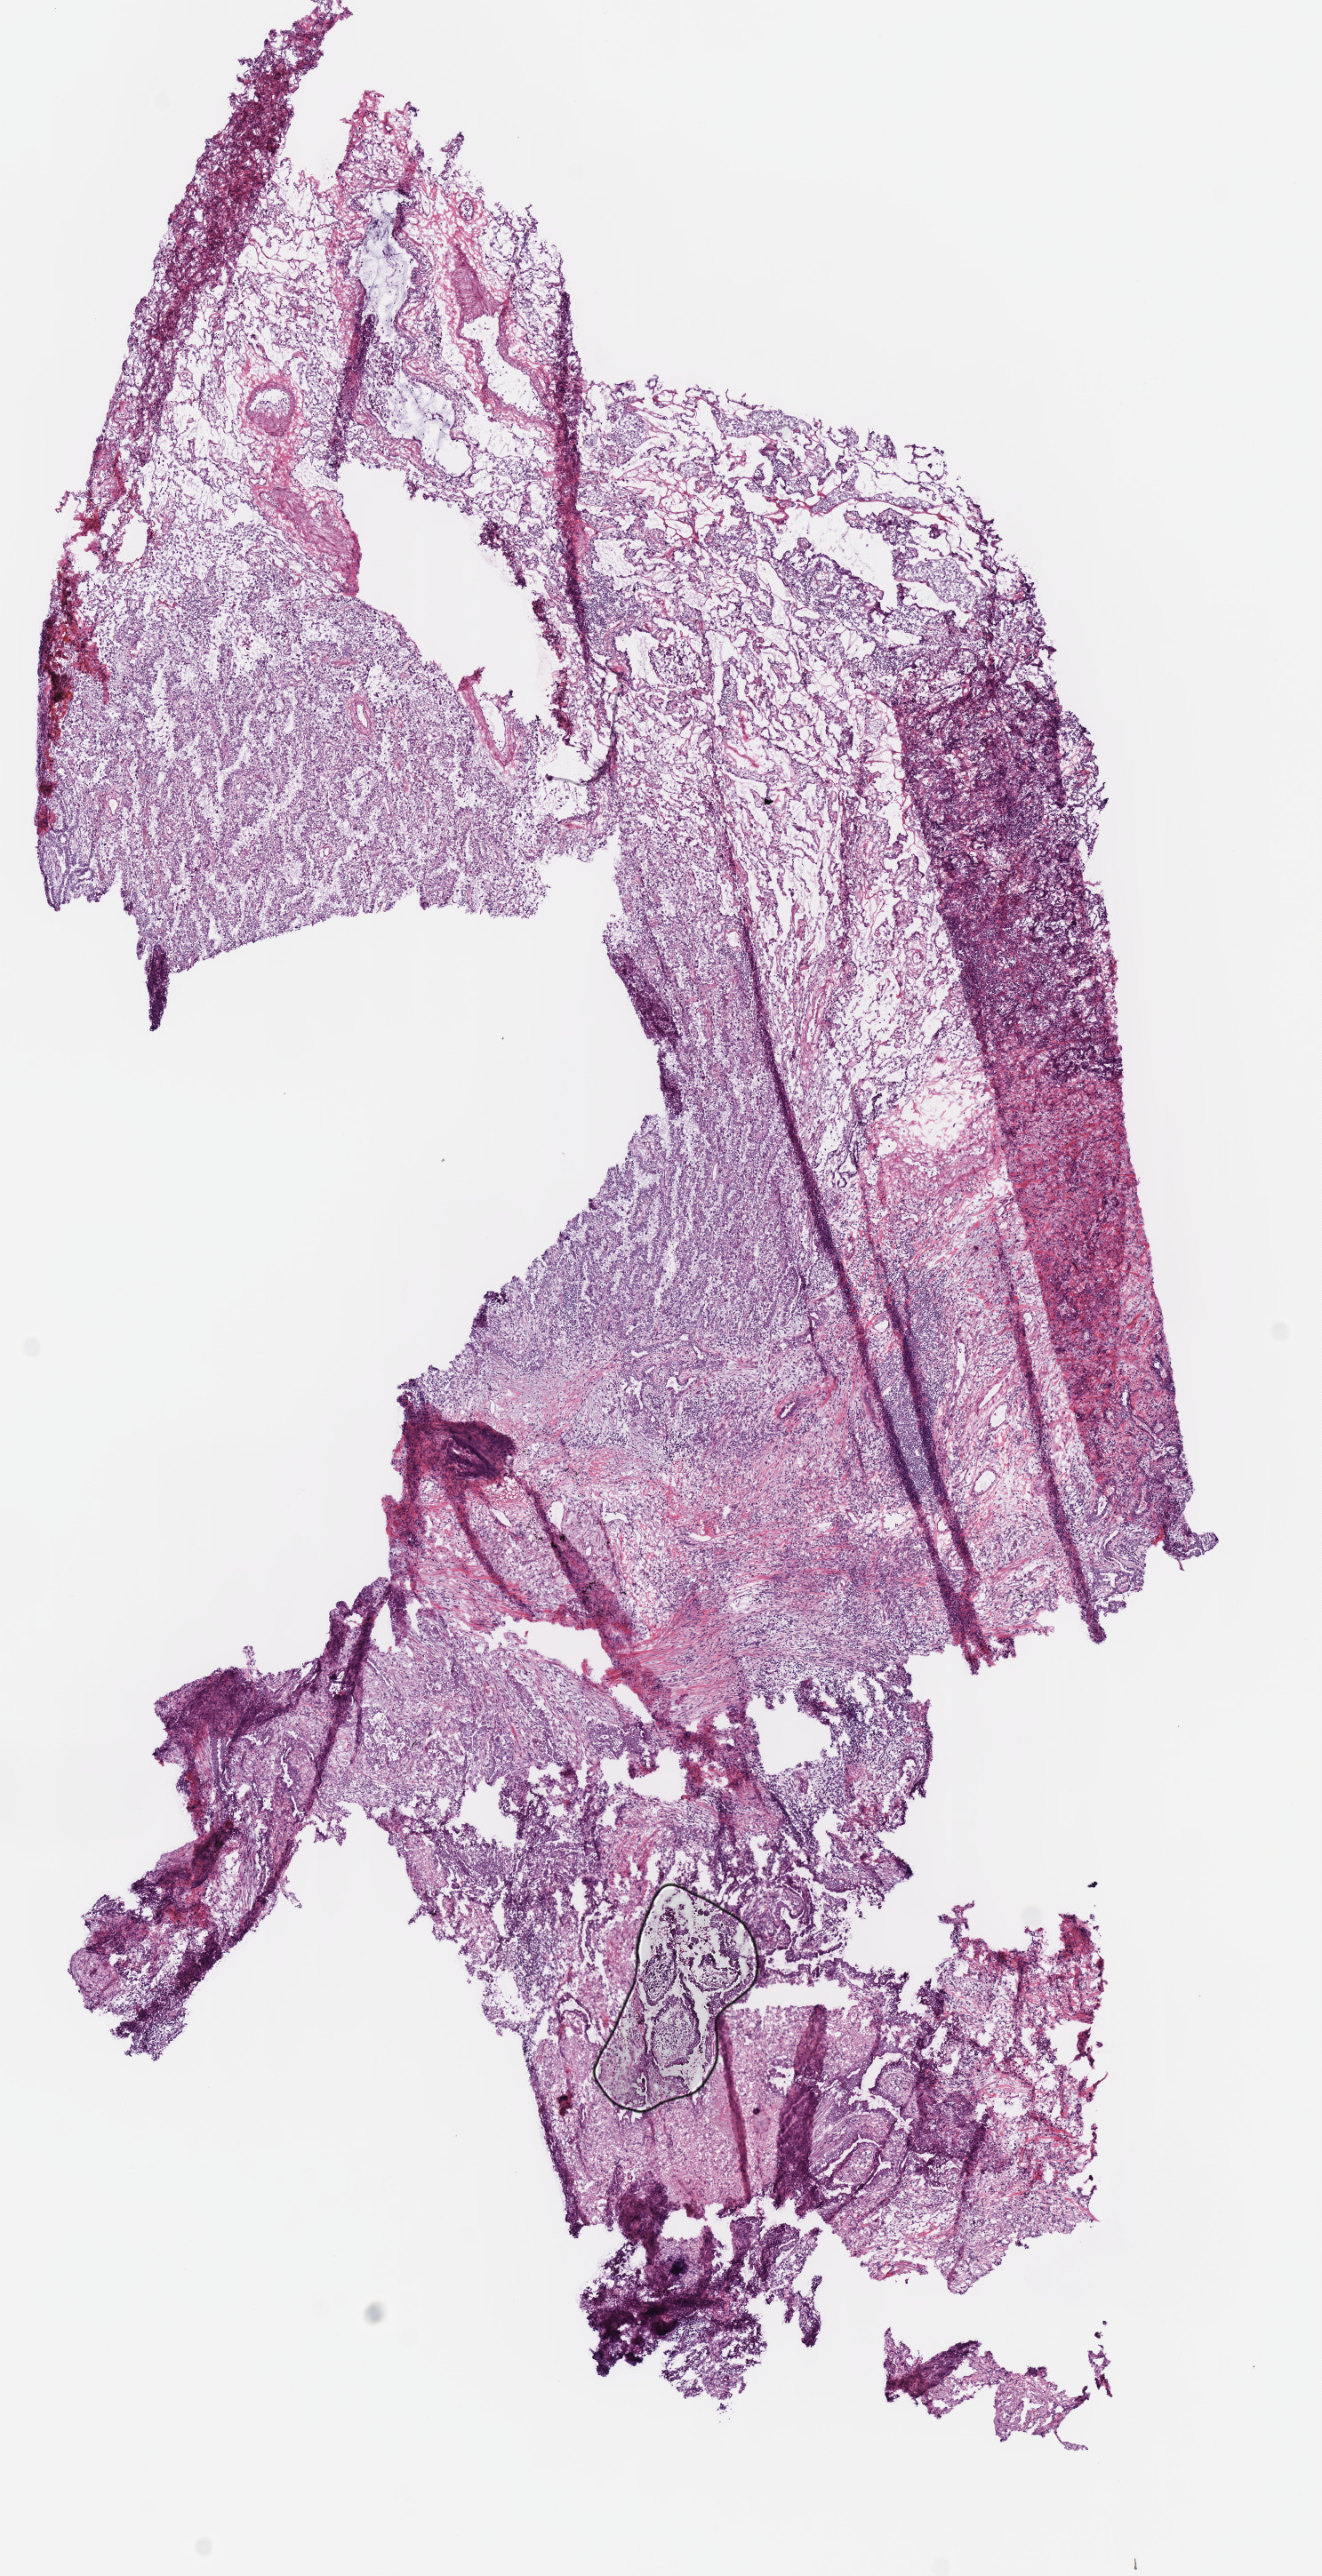
Whole-slide histology image, Hematoxylin and eosin (H&E) stained, a low-resolution overview of the entire scanned area, about 5.9 x 11.4 mm (acquisition: 40x scan). Frozen section. Sample: primary tumour, lung. Patient: female, age at initial diagnosis 75 years. Pathologist review of this section (percent, as recorded): tumour cells 50%, tumour nuclei 60%, normal cells 20%, stromal cells 30%, necrosis 0%.
Laterality: right. AJCC pathologic stage: IA (7th edition). Histologic diagnosis: Adenocarcinoma, NOS.